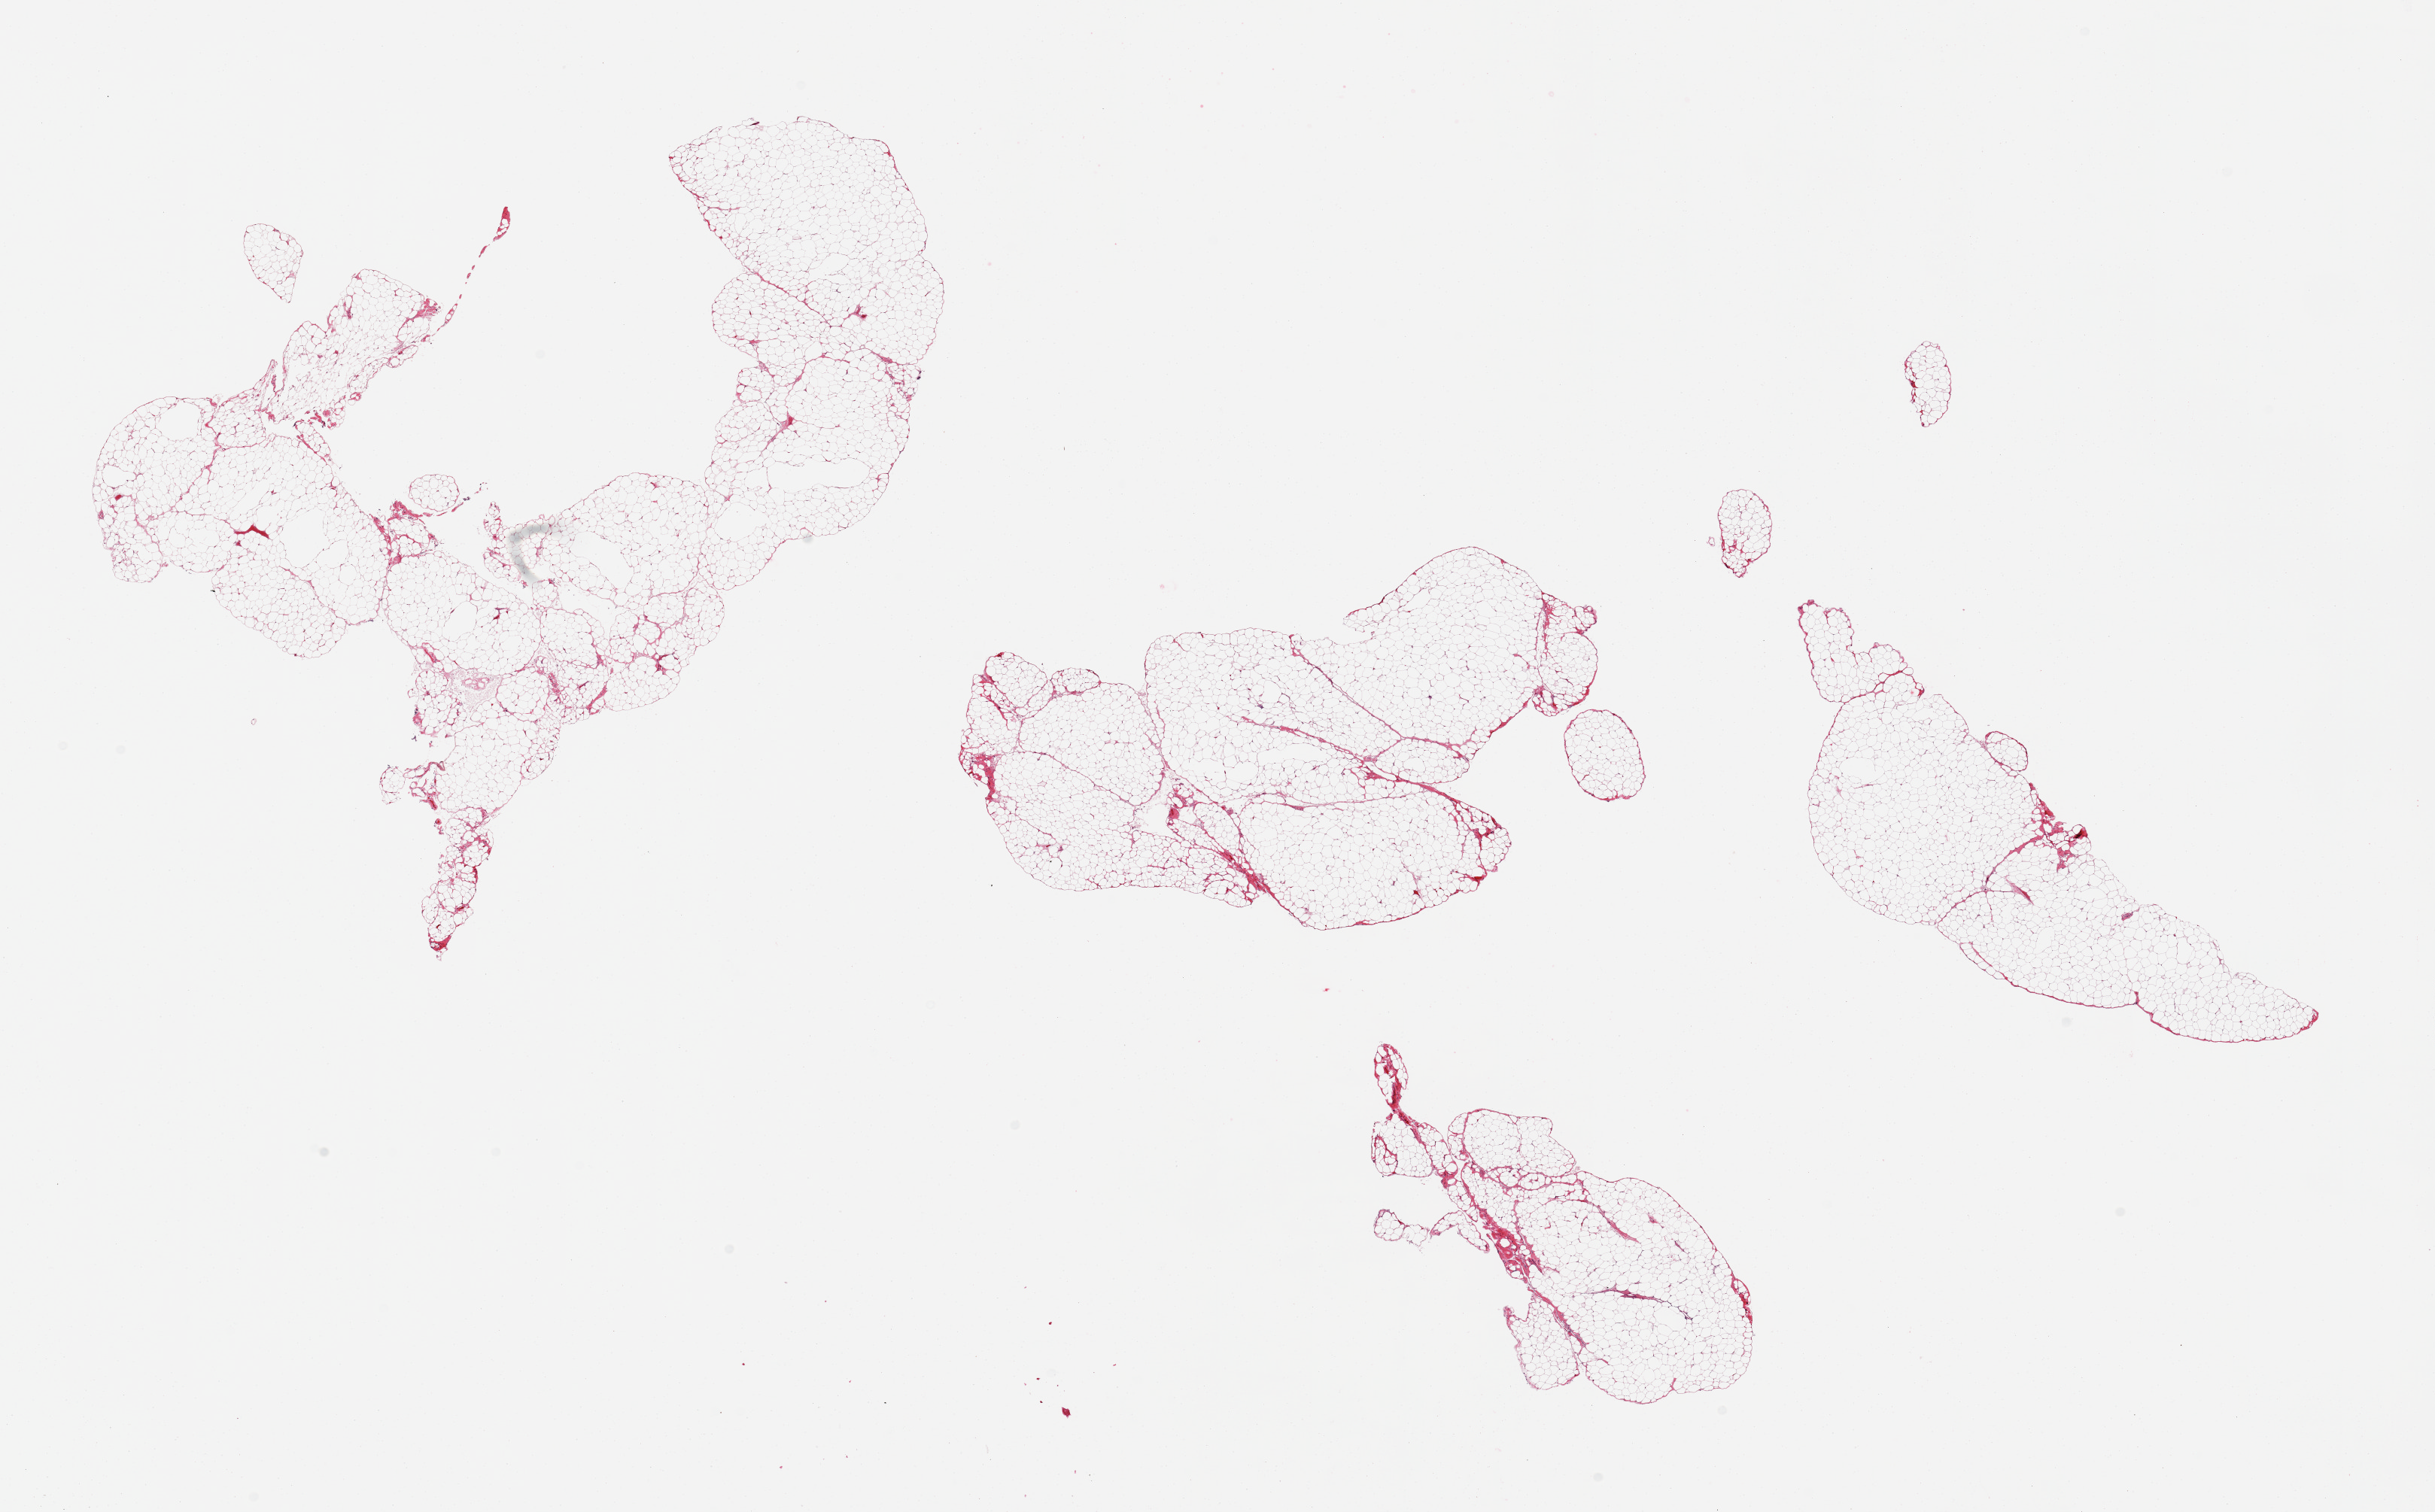
Whole-slide image, H&E stain — whole scanned area (about 25.6 x 15.9 mm) shown as a low-resolution overview, PAXgene-fixed, paraffin-embedded tissue, sampled site (target tissue): omentum, donor tissue sample. Male donor.
* reviewer comment on this tissue sample: 4 fragmented pieces